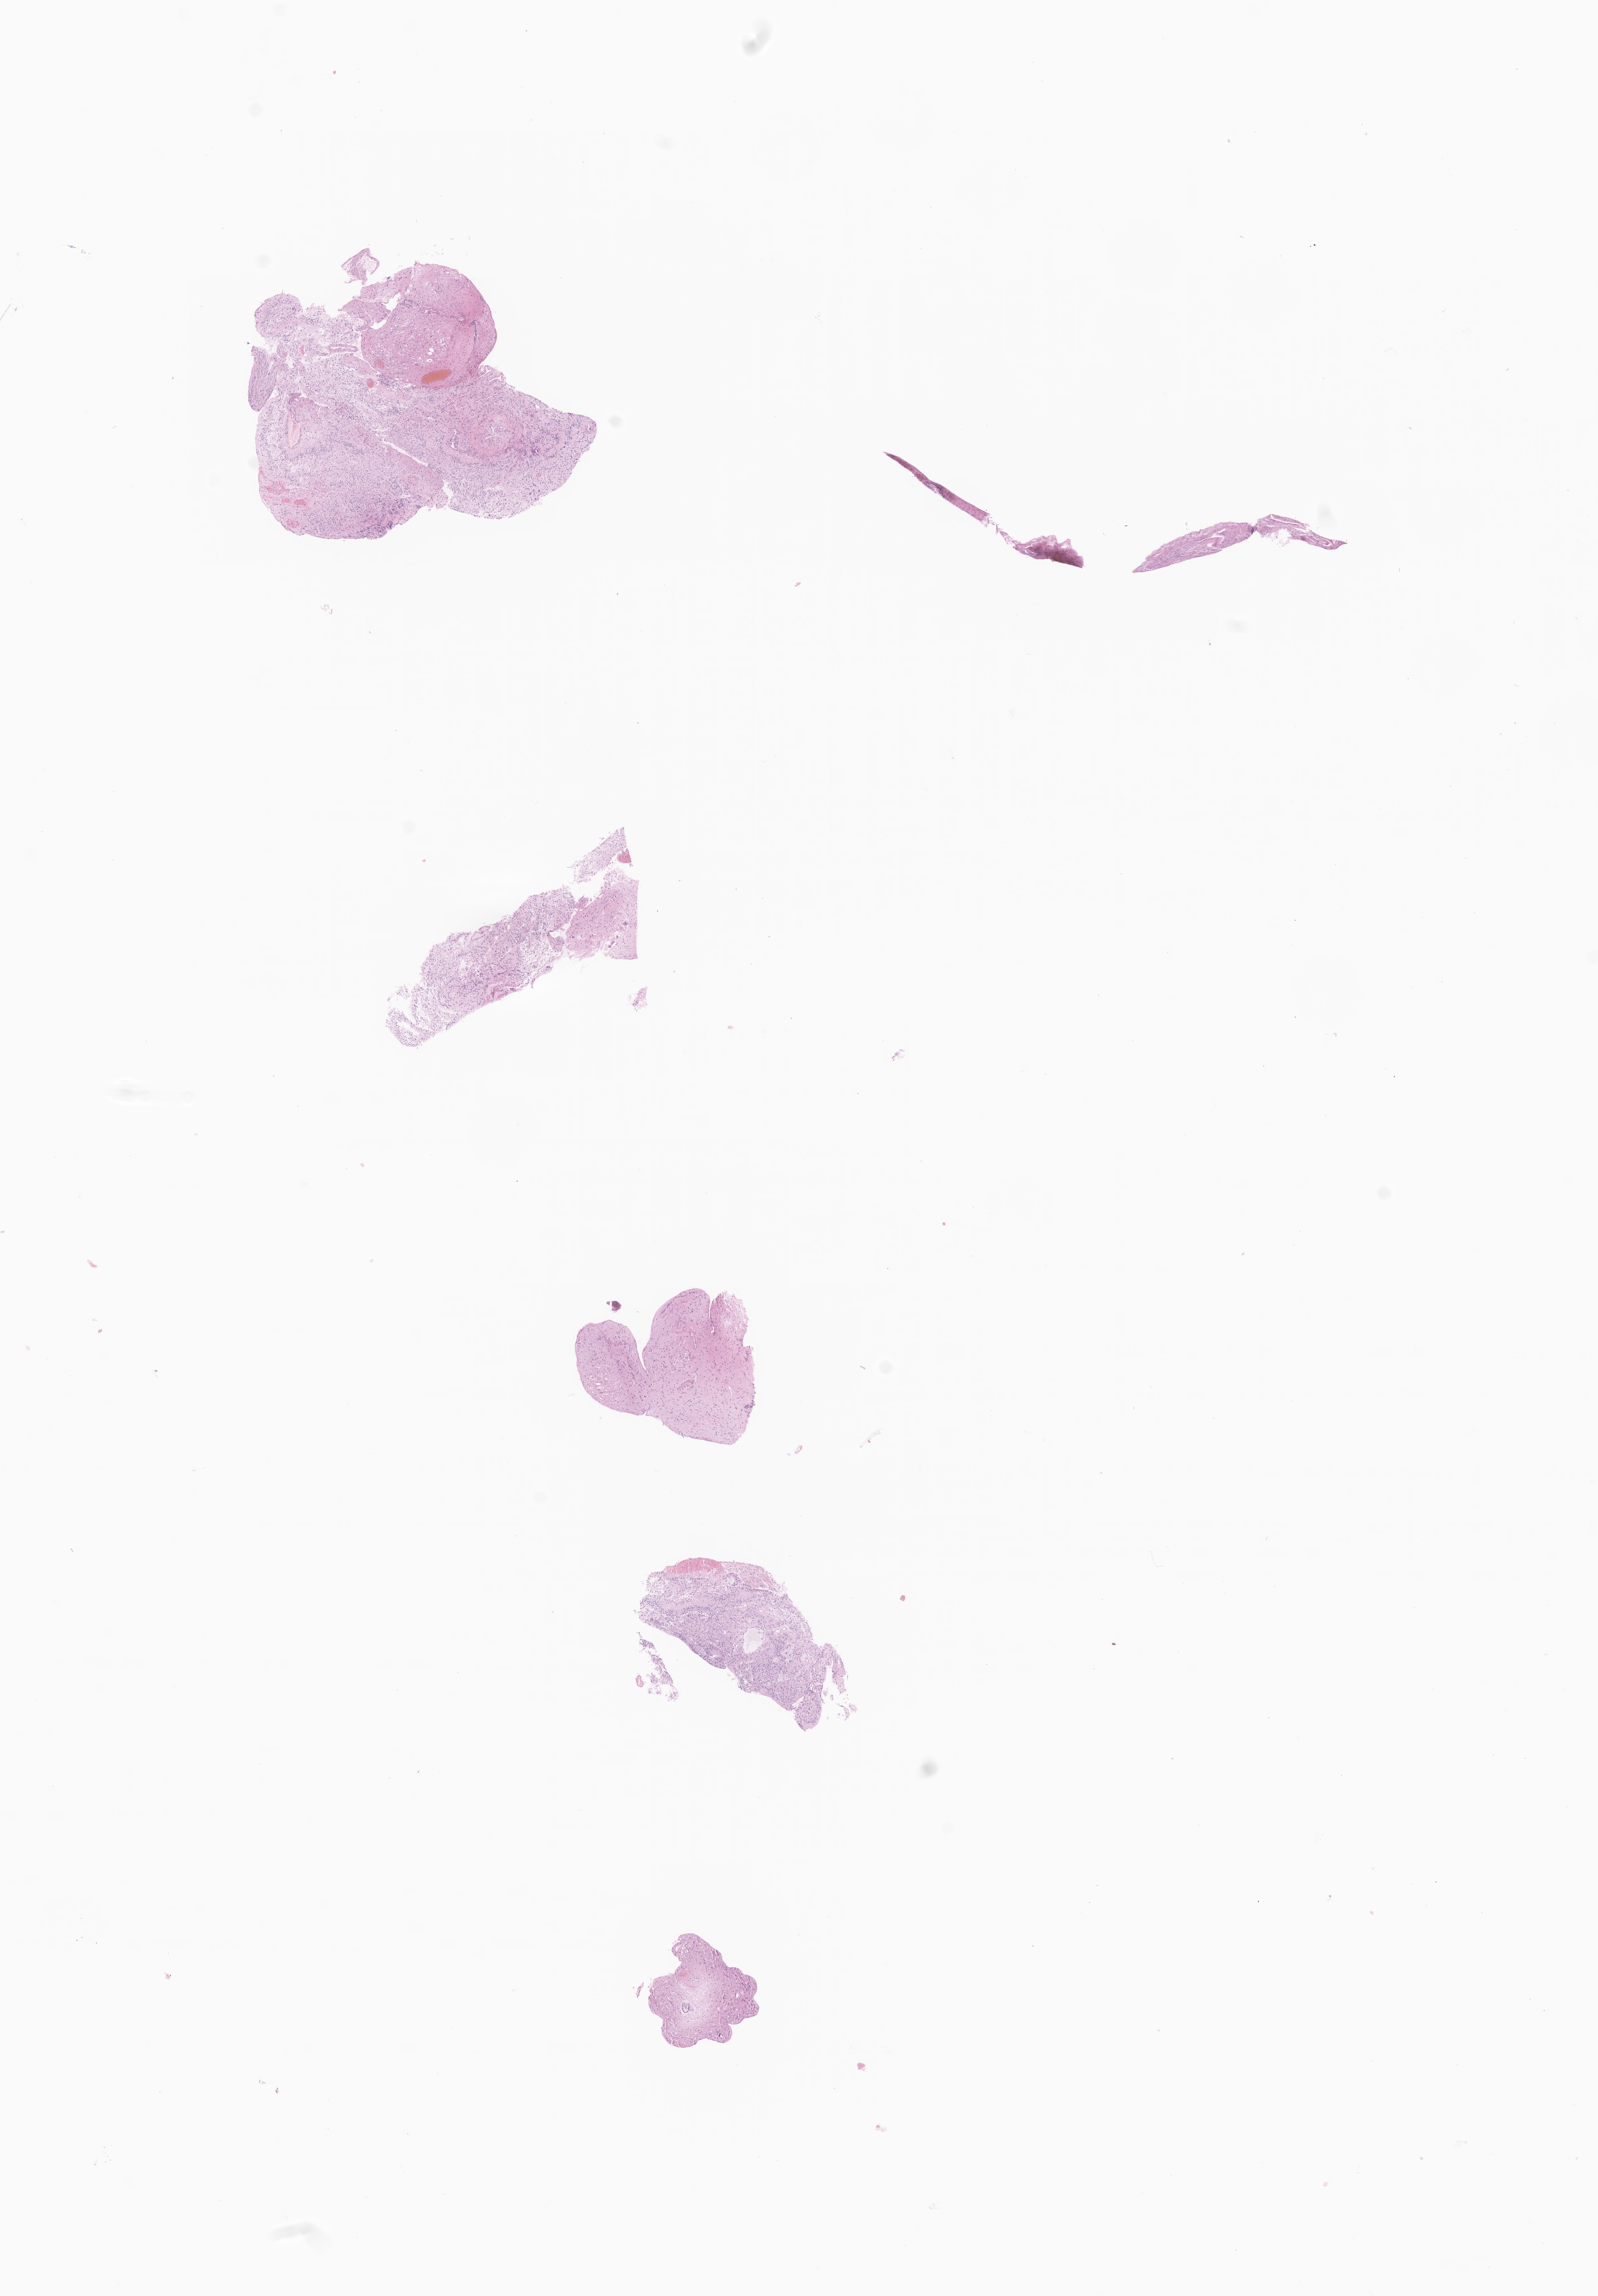
Digitized hematoxylin and eosin (H&E)-stained section of tumor tissue from the brain, whole scanned area (about 11.8 x 17.0 mm) shown as a low-resolution overview. FFPE section. Male patient, age 317 months.
Diagnosis (ICD-O-3 morphology term): Pilocytic astrocytoma.